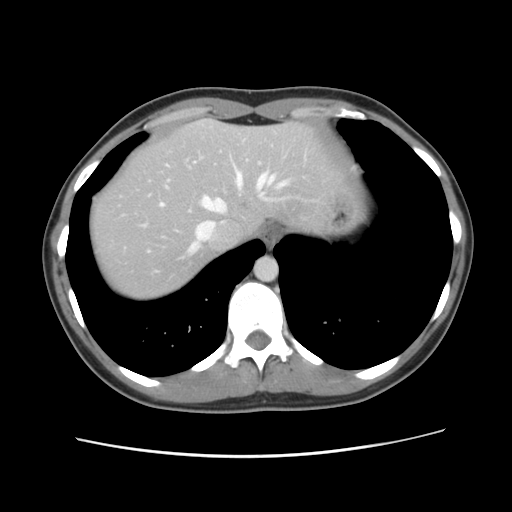
Contrast-enhanced abdominal CT, one axial slice; slice 102 of 134 in the series (ordered by position); soft-tissue window (W 400 / L 40 HU); 512 × 512 image matrix, field of view 339 × 339 mm. Female patient, age 33 years. Case-level facts recorded for this patient, not image findings: diagnosis: colorectal cancer liver metastases, imaged before liver resection; multiple liver metastases: yes.
Structures marked on this image (expert manual segmentation):
- hepatic veins: bounding box [x1, y1, x2, y2] px = [161, 166, 289, 253]
- liver: [89, 120, 341, 301]
- planned liver remnant (the part of the liver to remain after resection): [89, 120, 341, 301]